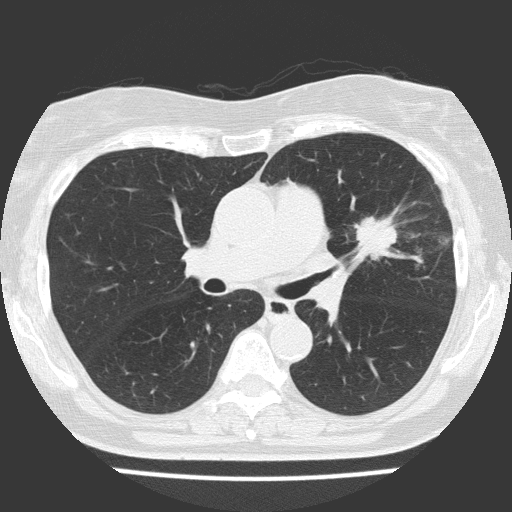
Chest CT (low-dose screening protocol), one axial image. Baseline annual screen. Lung window (W 1500 / L -600 HU). 2 mm slice thickness. Lung (sharp) reconstruction kernel (FC51). Slice 64 of 151 in the series. 512 × 512 image matrix. Female participant, aged 70 years at enrolment. Current smoker at enrolment.
• Expert reader's lesion annotation, bounding box (x1, y1, x2, y2) in pixels: (326, 192, 432, 282).
• The screening reader recorded 2 non-calcified nodules or masses ≥4 mm on this exam (left upper lobe, right upper lobe); which of them this box marks is not recorded.
• Official screen result: positive, change unspecified: nodule(s) >= 4 mm or enlarging nodule(s), mass(es), or other non-specific abnormalities suspicious for lung cancer.
• Later outcome: lung cancer diagnosed 25 days after this screen — adenocarcinoma, NOS, left upper lobe, poorly differentiated (G3), stage IV (AJCC 6th edition), 30 mm at pathology.